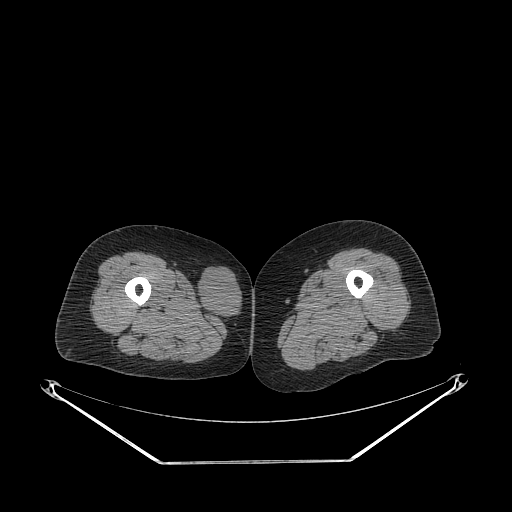
CT of an extremity soft-tissue mass (from a PET/CT study), one axial slice. Position 234 of 311 along the scan axis. Reconstruction kernel STANDARD. 140 kVp. Soft-tissue window (W 400 / L 40 HU). 3.75 mm slice thickness. 512 × 512 image matrix. Female patient. Case-level facts recorded for this patient, not image findings: histological type: leiomyosarcoma; grade: intermediate; site of the primary tumour: parascapusular.
Structures marked on this image (expert contour drawn on MRI and transferred to this co-registered scan by the dataset authors):
- gross tumour volume including surrounding oedema: bounding box [x1, y1, x2, y2] px = [198, 267, 243, 321]
- gross tumour volume (mass): [198, 267, 243, 321]